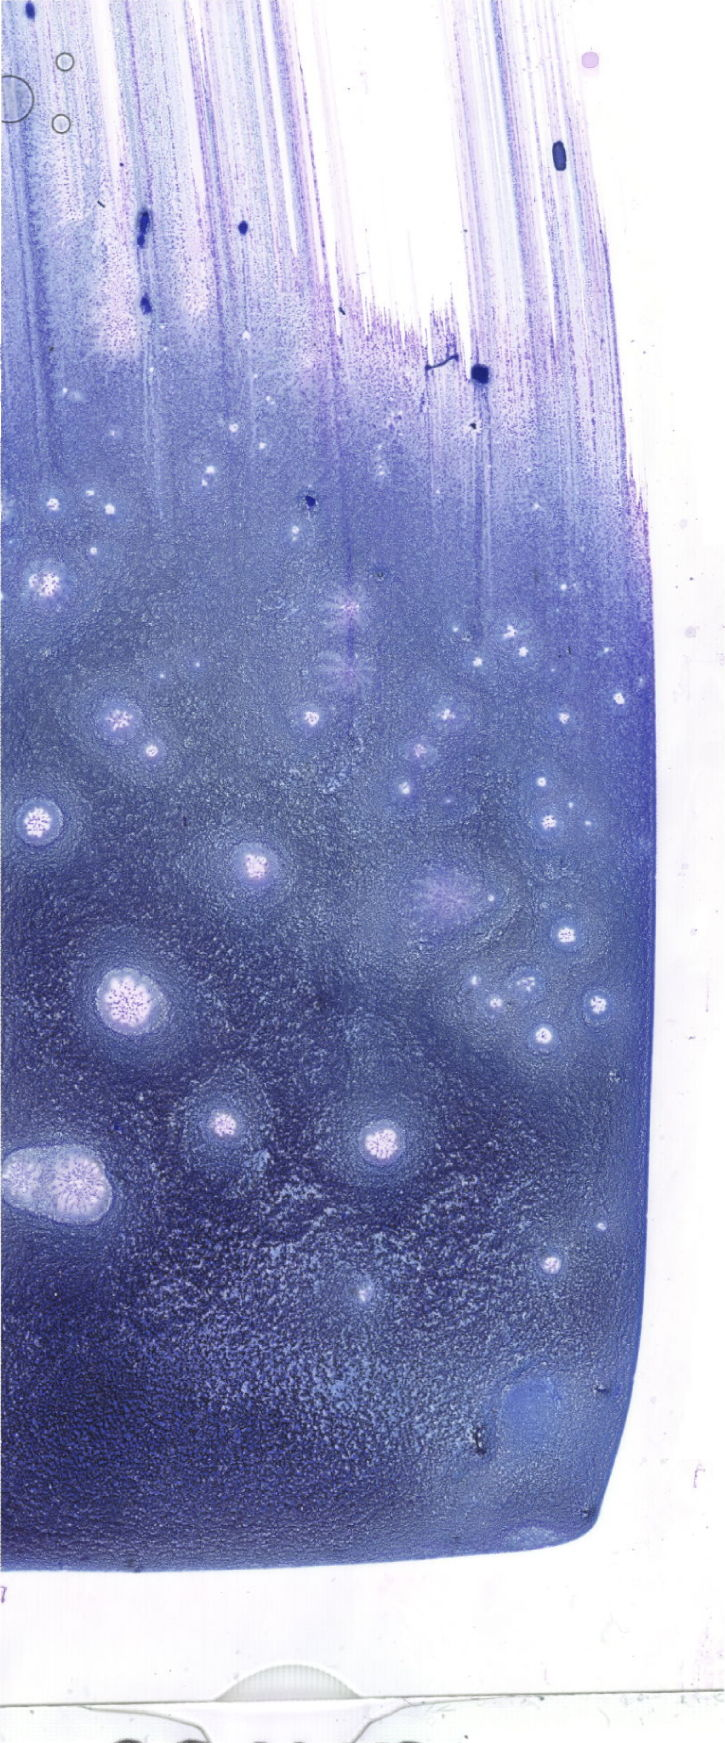
Bone marrow aspirate smear, May-Grünwald-Giemsa (MGG) stain, whole-slide image, shown as a low-resolution overview of the whole scanned area (about 20.6 x 49.4 mm).
Diagnosis: Acute Myelomonocytic Leukemia with Abnormal Eosinophils.